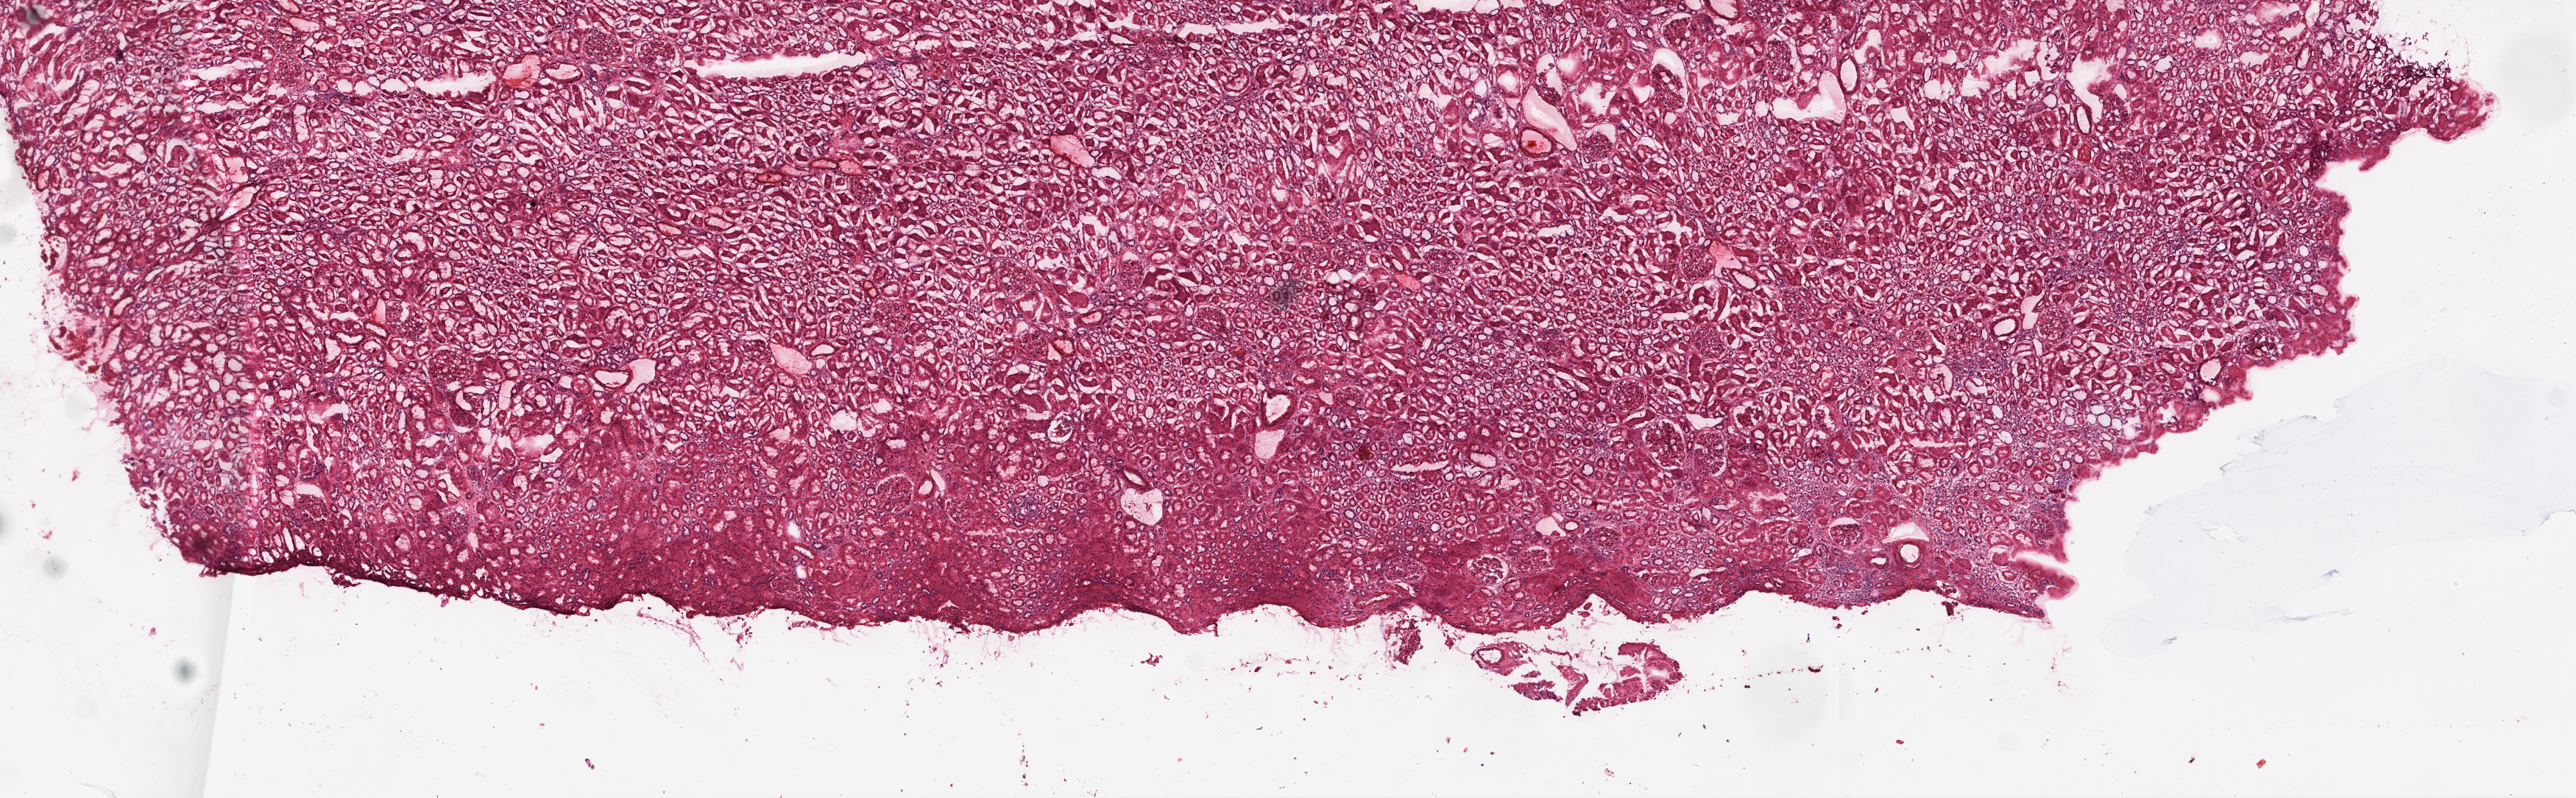
H&E whole-slide image, whole scanned area (about 14.0 x 4.3 mm) shown as a low-resolution overview, frozen section from the top of the tissue portion, solid tissue normal (non-tumour tissue) sample from the kidney. Patient: female, age at initial diagnosis 73 years.
This section: solid tissue normal sample (biorepository sample class). Patient diagnosis: Clear cell adenocarcinoma, NOS.